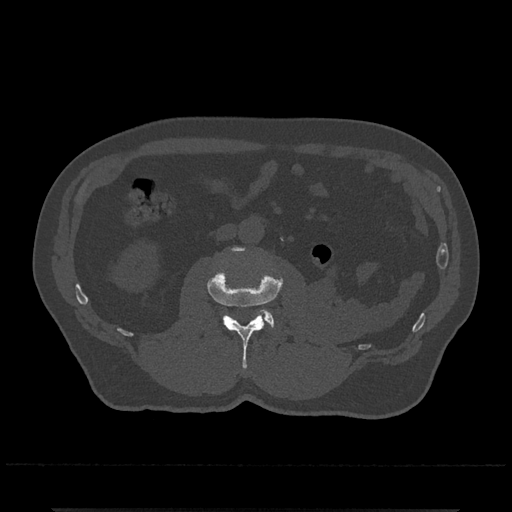
CT including the spine, one axial slice. Position 277 of 797 along the scan axis. Bone window (W 1800 / L 400 HU). 0.5 mm slice thickness. 512 × 512 image matrix. Patient: male, 67 years. Case-level facts recorded for this patient, not image findings: primary cancer: prostate.
Annotated regions visible in this slice (semi-automatically segmented with operator editing):
- L2 vertebra: bounding box (x1, y1, x2, y2) in pixels: (207, 247, 283, 369)
- L3 vertebra: (258, 310, 274, 327)